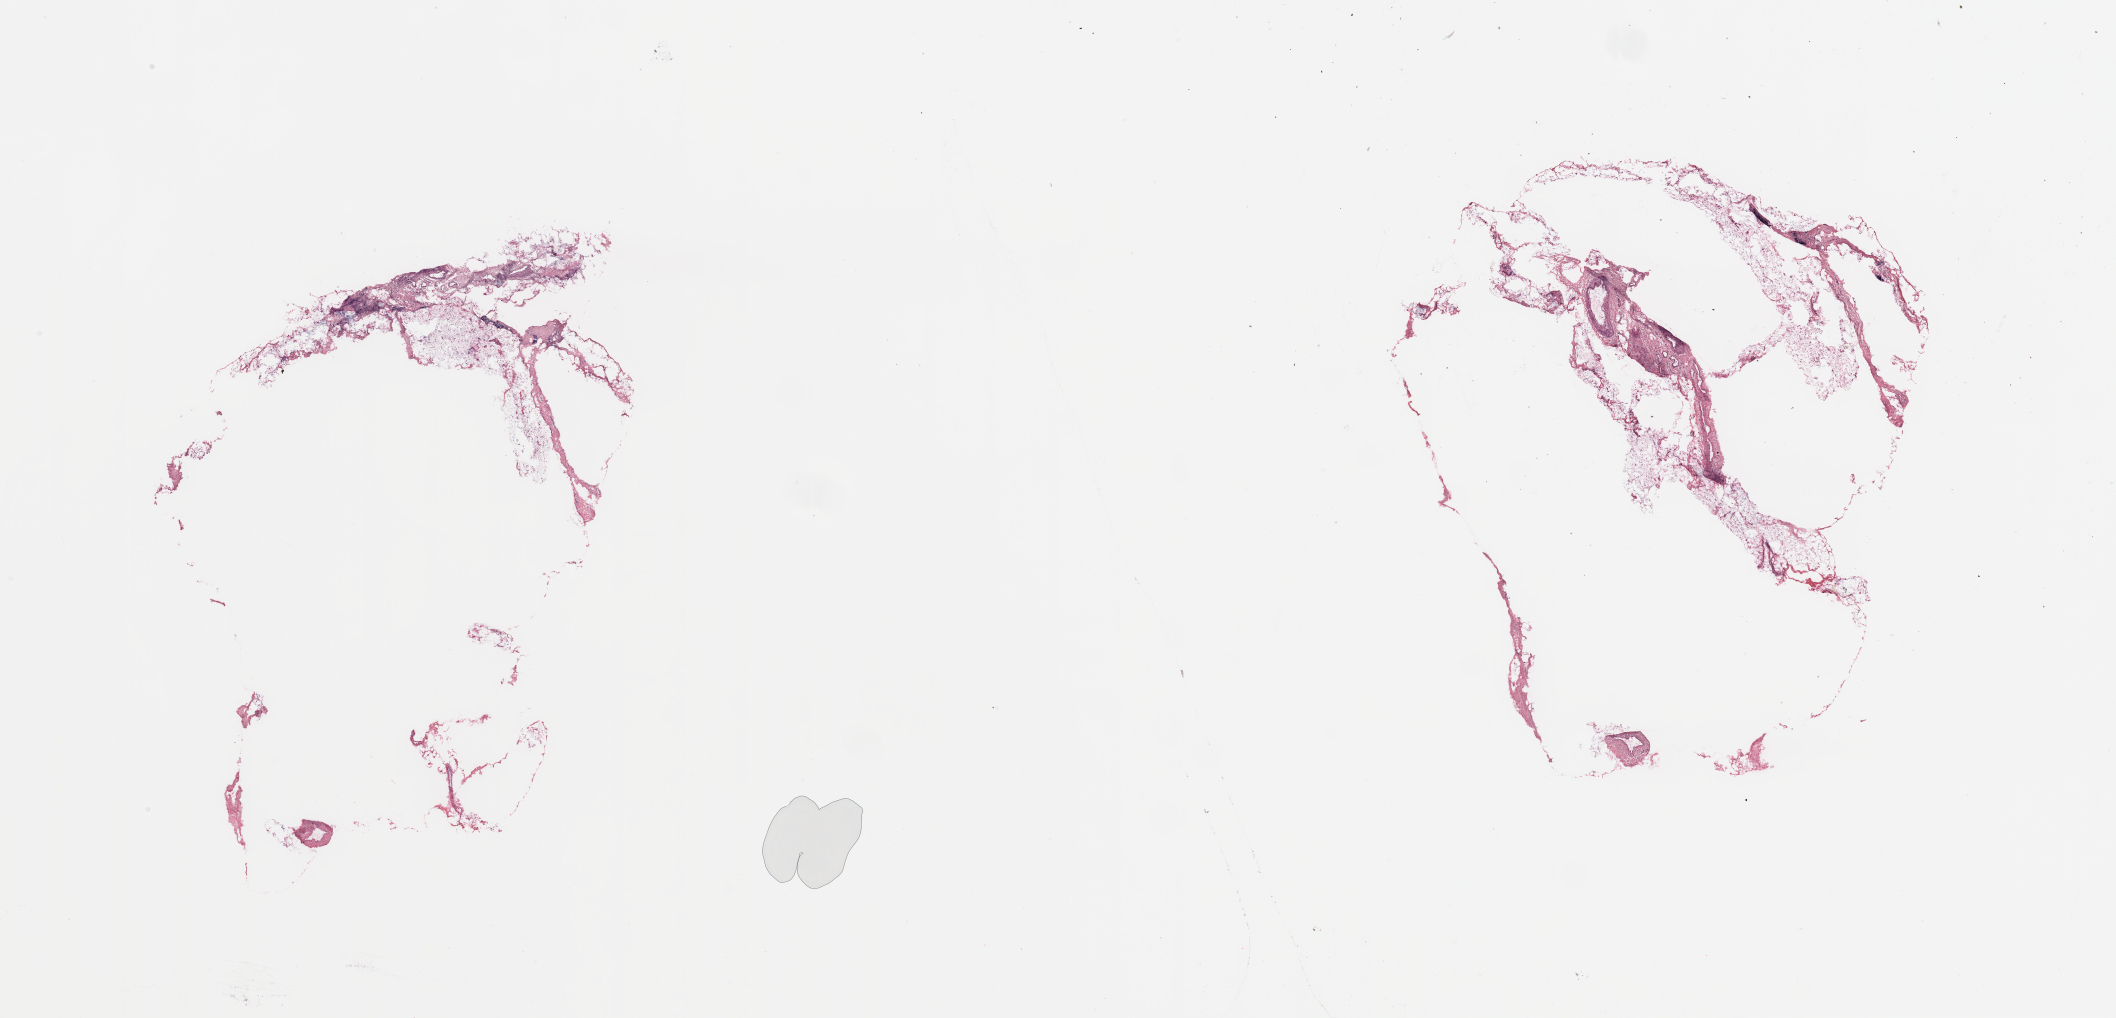
Digitized H&E tissue section (whole slide) — low-resolution overview of the scanned area, about 33.5 x 16.1 mm; breast, tumour tissue. Patient: female, age 55 years.
AJCC pathologic stage: IIA. Histologic diagnosis: Infiltrating duct carcinoma, NOS.